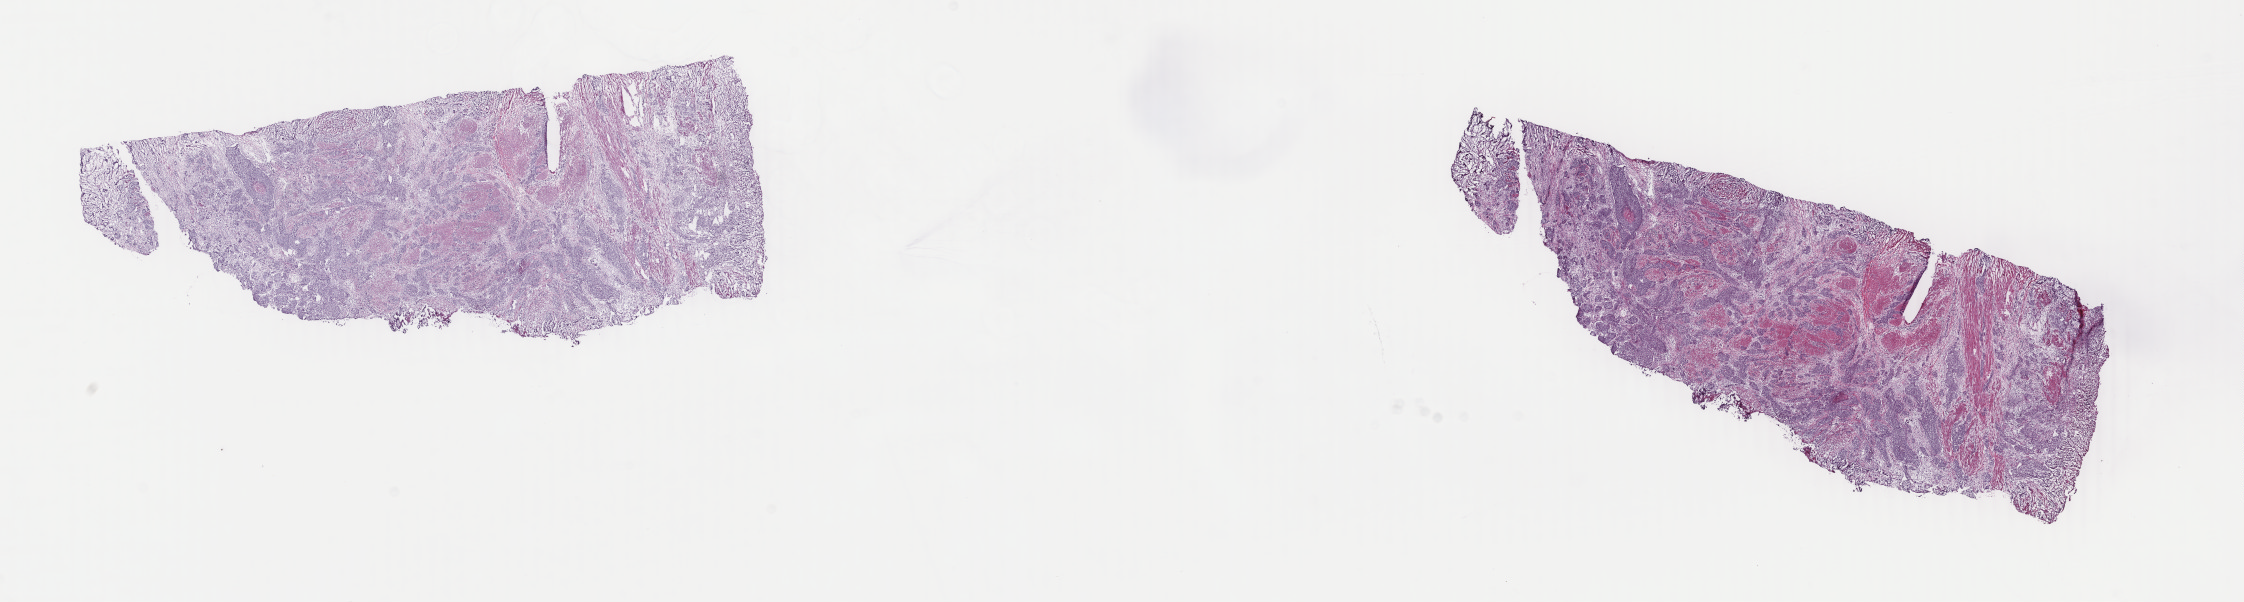
Whole-slide histology image, H&E, whole scanned area (about 35.7 x 9.6 mm, acquisition: 40x scan) shown as a low-resolution overview; frozen section from the top of the tissue portion; sample: primary tumour, bladder. Female patient; age at initial diagnosis 74 years. Histologic grade: high grade. Composition of this section per pathologist review: tumour cells 75%, tumour nuclei 75%, normal cells 0%, stromal cells 22%, necrosis 3%. Infiltration values recorded for this section: lymphocyte infiltration 2%, monocyte infiltration 1%, neutrophil infiltration 1%.
Pathologic diagnosis: Transitional cell carcinoma. AJCC pathologic stage: IV.